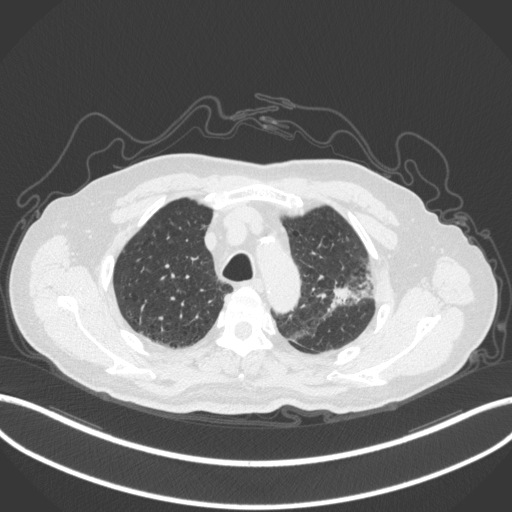
Chest CT, one axial slice. Slice 237 of 331 in the series (ordered by position). Reconstruction kernel B31f. Lung window (W 1500 / L -600 HU). 1 mm slice thickness. 512 × 512 image matrix, field of view 400 × 400 mm. Patient: male, 79 years. From the clinical record (not read from this slice): clinical TNM (as recorded): T2a N1 M1; histopathological grade: G3.
Outlined on this slice (bounding box drawn by a radiologist):
- lung tumour (recorded histology: adenocarcinoma): bounding box <312,269,378,316> (left, top, right, bottom; pixels)